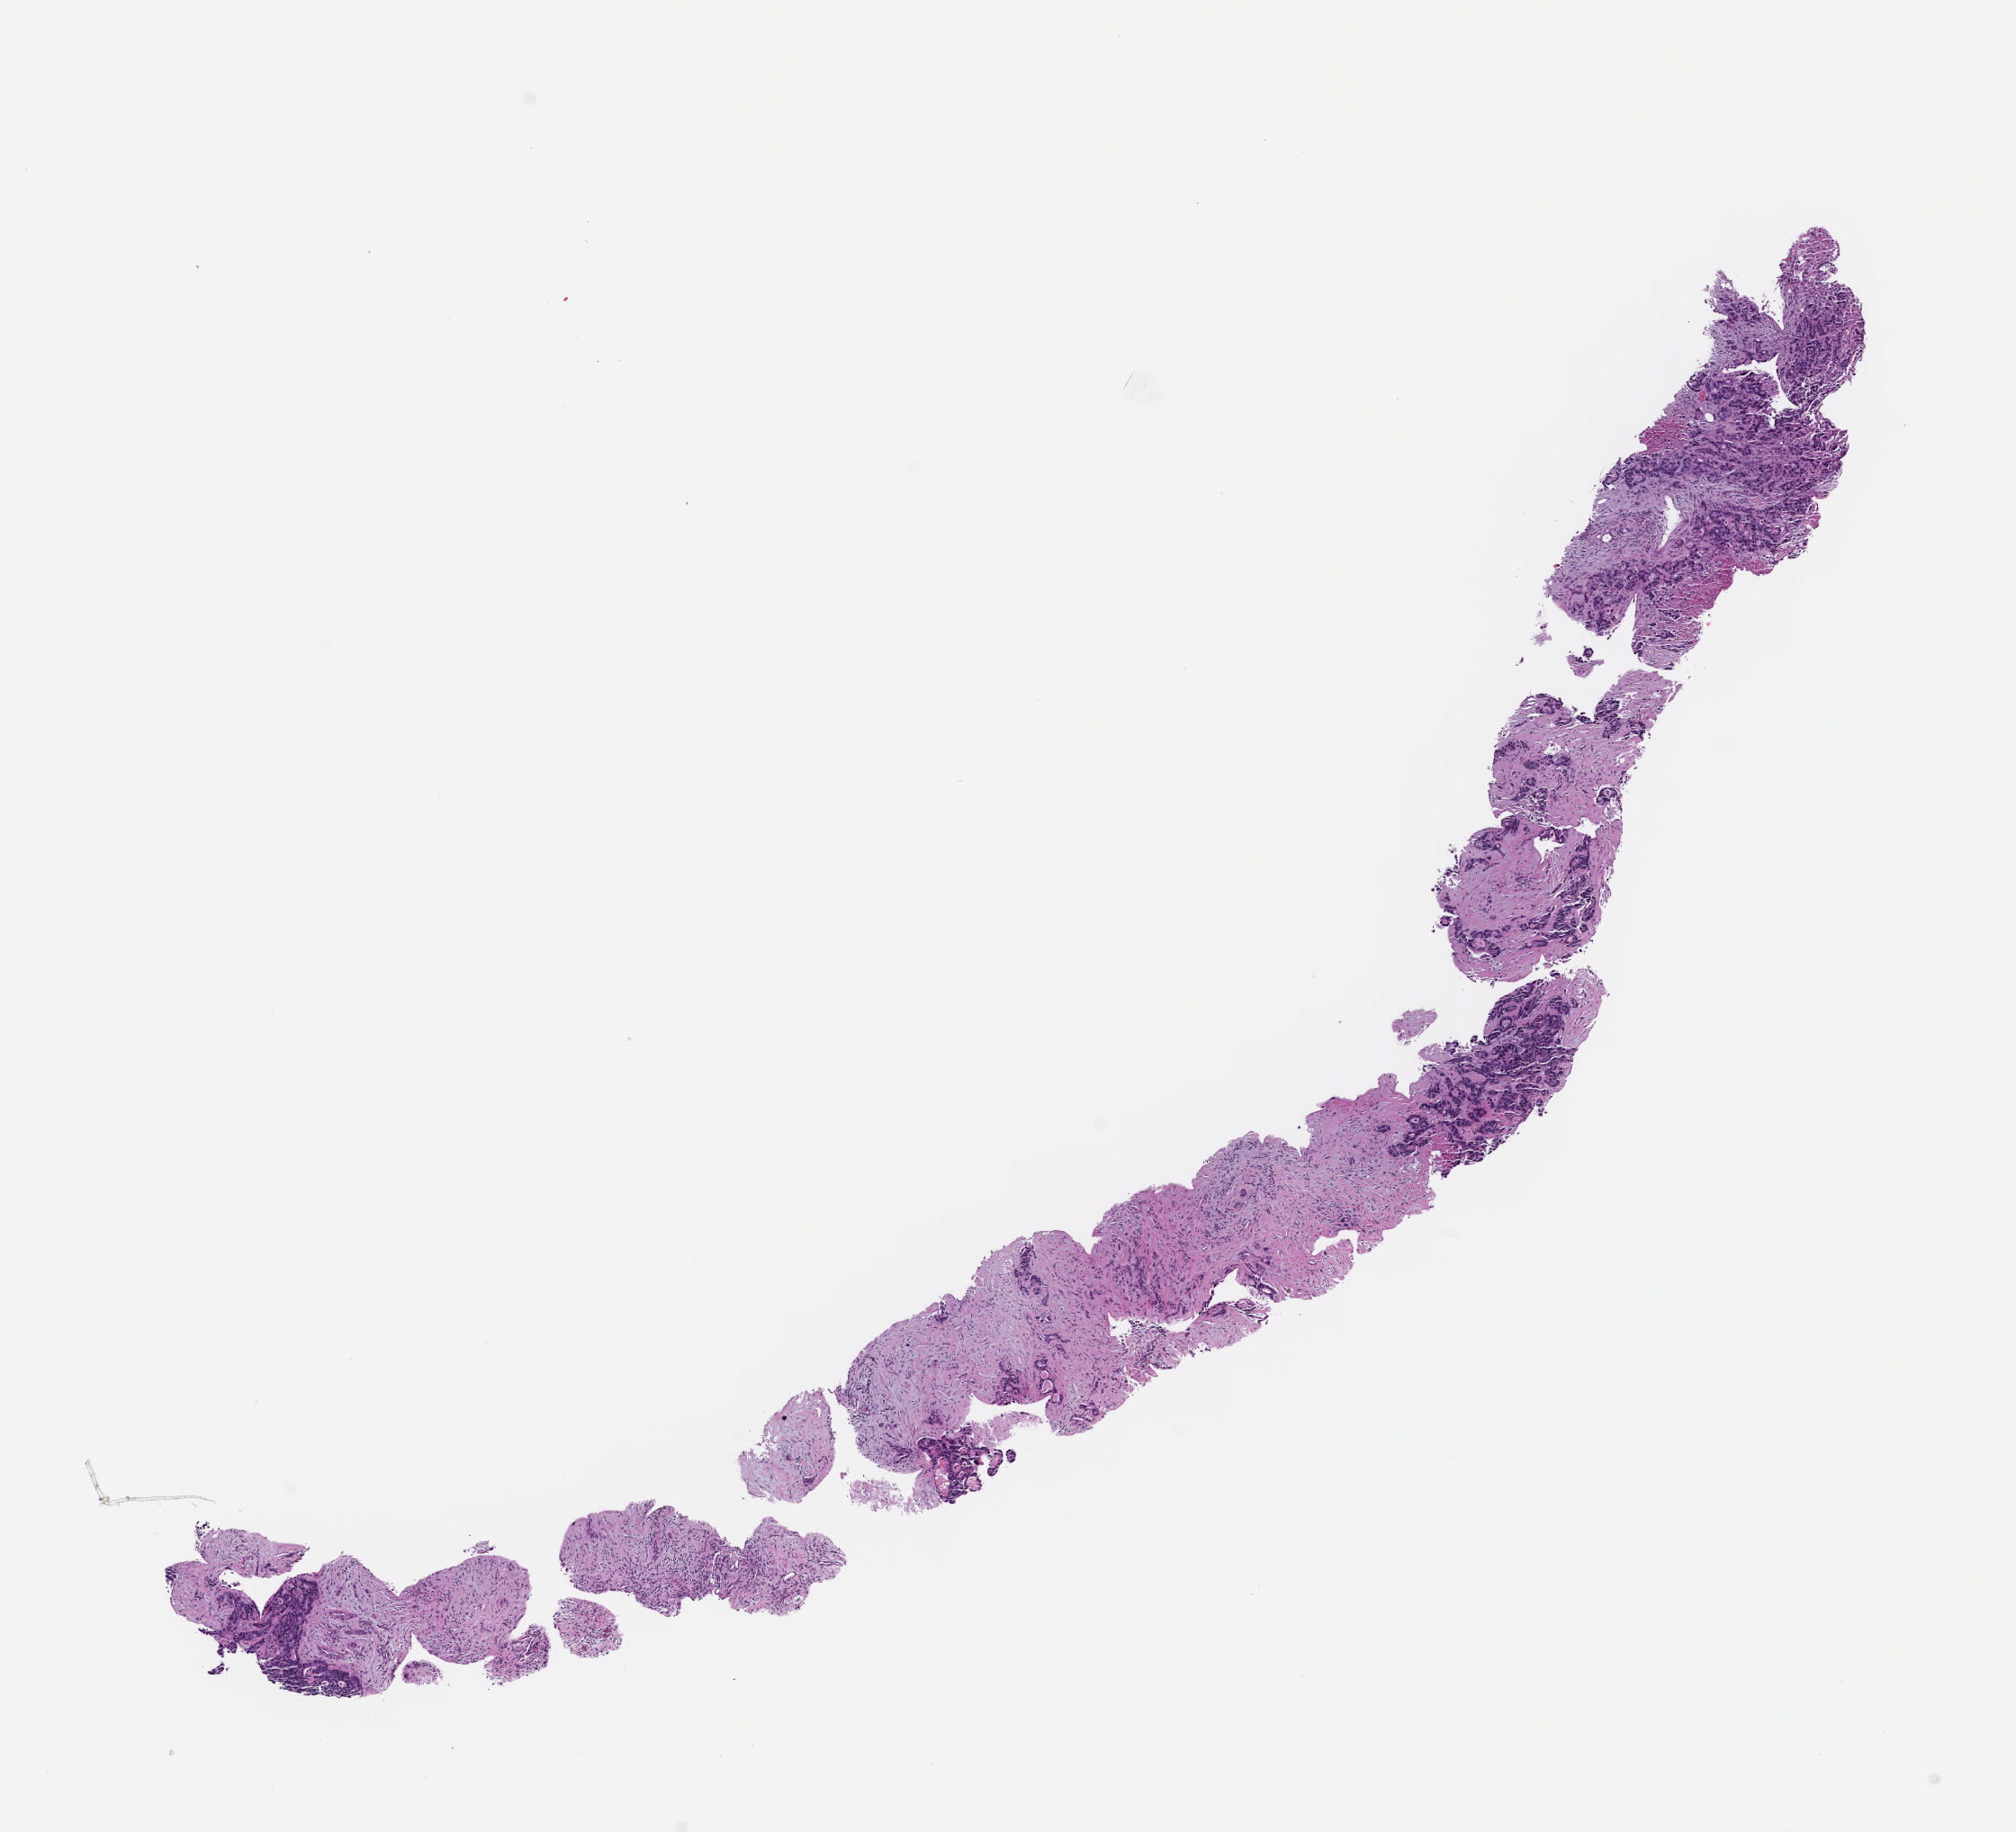
Hematoxylin and eosin (H&E) whole-slide image, a low-resolution overview of the entire scanned area, about 9.0 x 8.2 mm; formalin-fixed paraffin-embedded section; specimen time point: collected at disease progression. Male patient.
This section: metastatic tumor tissue. Patient diagnosis (primary): Colorectal Carcinoma.